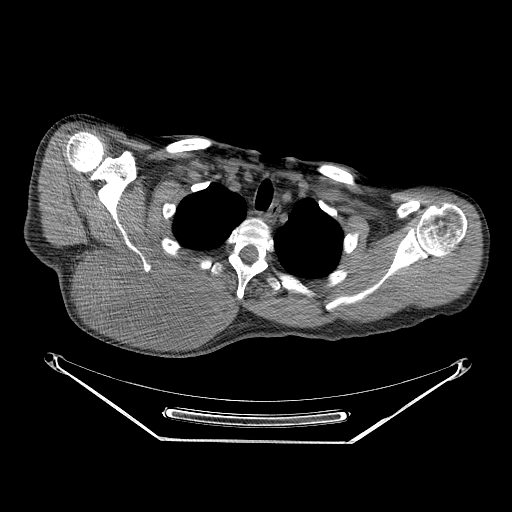
CT of an extremity soft-tissue mass (from a PET/CT study), one axial slice. Position 200 of 267 along the scan axis. Reconstruction kernel STANDARD. Soft-tissue window (W 400 / L 40 HU). 3.75 mm slice thickness. 512 × 512 image matrix, field of view 500 × 500 mm. Male patient. Case-level facts recorded for this patient, not image findings: histological type: pleiomorphic spindle cell undifferentiated; grade: high; site of the primary tumour: right parascapusular.
Structures marked on this image (expert contour drawn on MRI and transferred to this co-registered scan by the dataset authors):
- gross tumour volume including surrounding oedema: box from (x=78, y=249) to (x=234, y=334) px
- gross tumour volume (mass): (x=78, y=251)–(x=220, y=334)